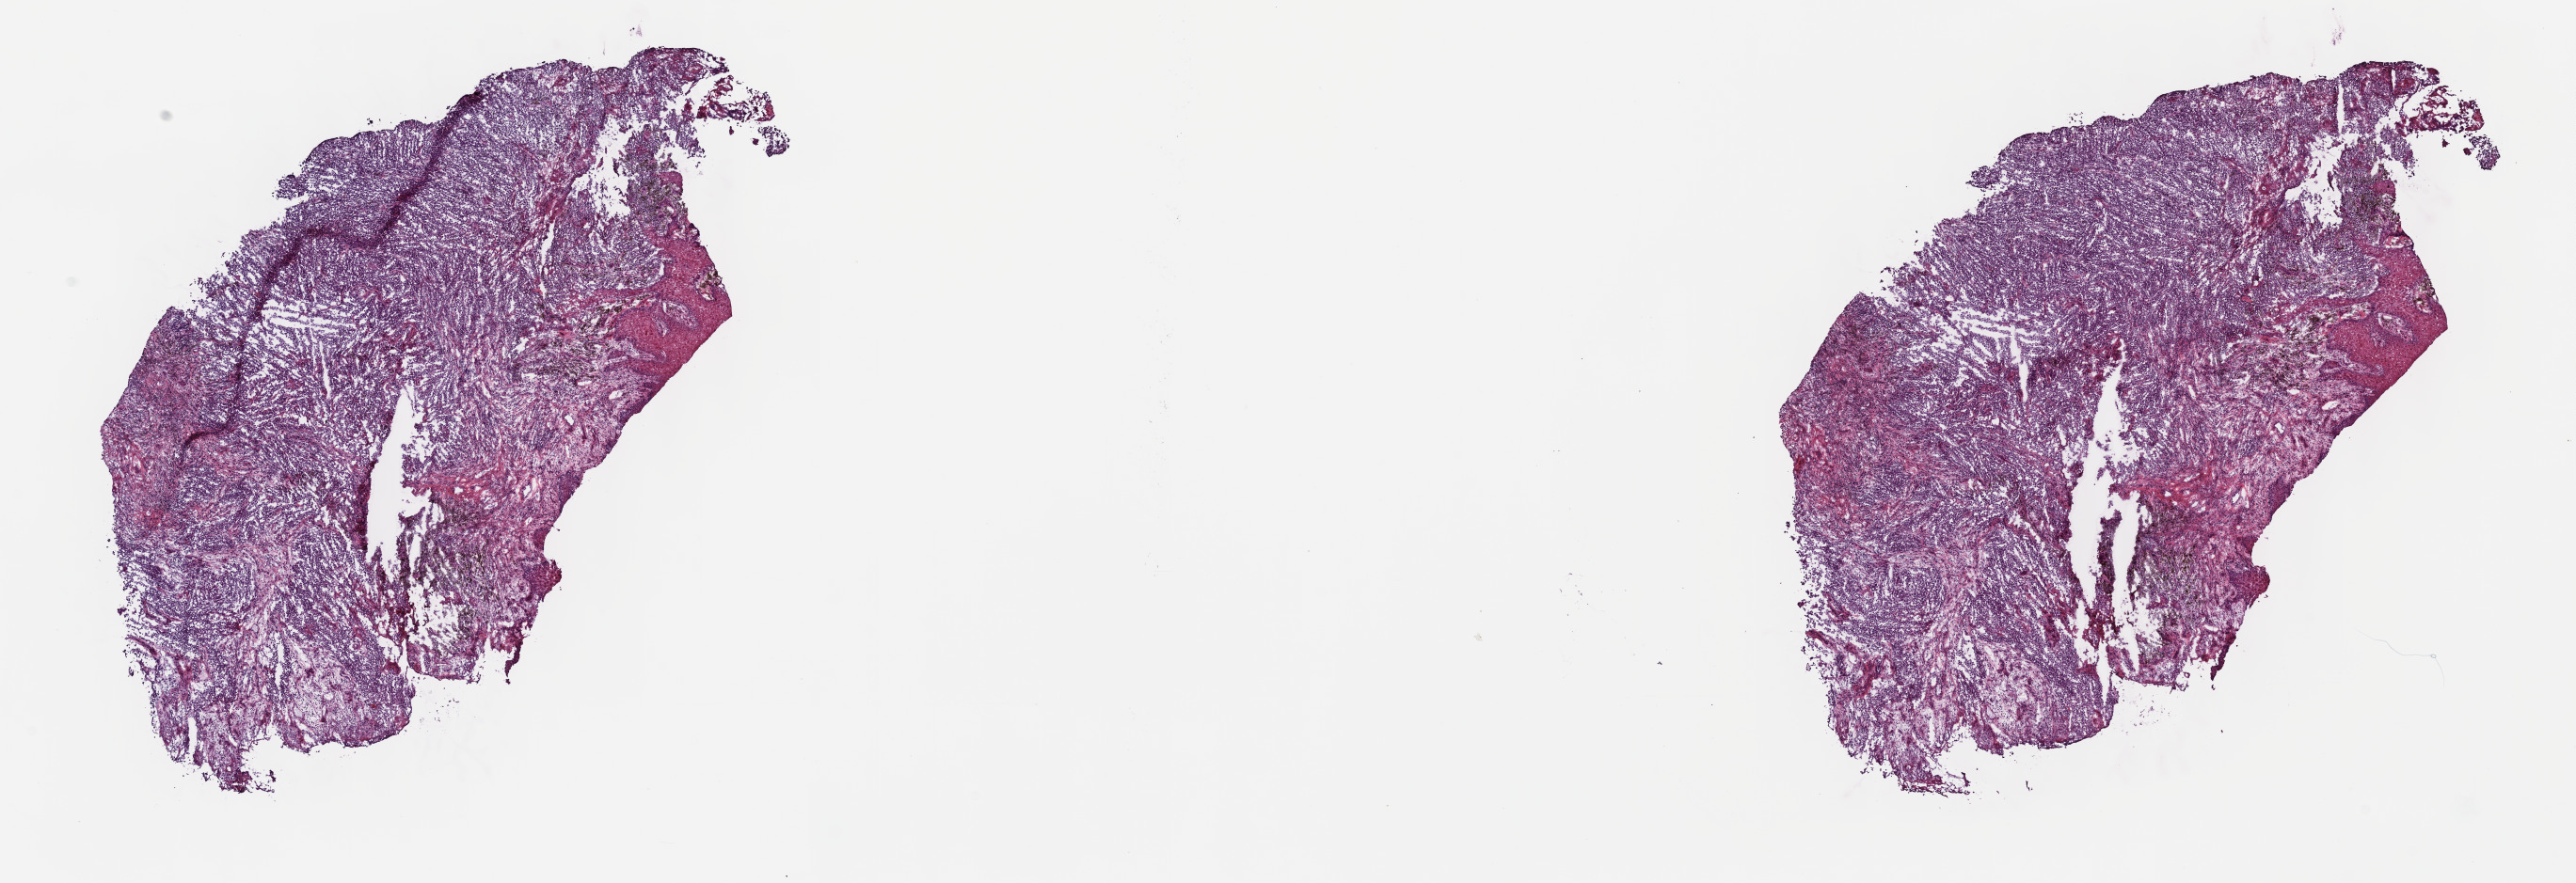
Digitized H&E-stained tissue section (whole slide), whole scanned area (about 22.1 x 7.6 mm) shown as a low-resolution overview. Frozen section from the top of the tissue portion. Primary tumour sample from the skin. Female, age 76 years at initial diagnosis. Pathologist review of this section (percent, as recorded): tumour cells 100%, tumour nuclei 80%, normal cells 0%, stromal cells 0%, necrosis 0%. Infiltration values recorded for this section: lymphocyte infiltration 2%, monocyte infiltration 0%, neutrophil infiltration 0%.
AJCC pathologic stage: IIC (7th edition). TNM: T4b N0 M0. Pathologic diagnosis: Epithelioid cell melanoma.